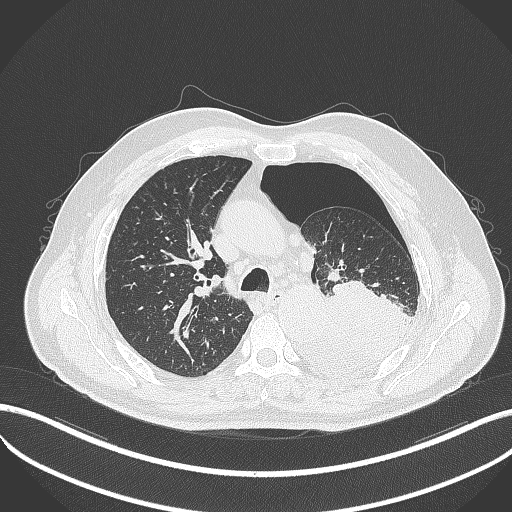
Chest CT, one axial slice. Slice 353 of 464 in the series (ordered by position). Reconstruction kernel B70f. 120 kVp. Lung window (W 1500 / L -600 HU). 1 mm slice thickness. 512 × 512 image matrix. Patient: male, 76 years. From the clinical record (not read from this slice): clinical TNM (as recorded): T3 N0 M1b.
Annotated regions visible in this slice (bounding box drawn by a radiologist):
- lung tumour (recorded histology: adenocarcinoma): bounding box <288,279,415,380> (left, top, right, bottom; pixels)